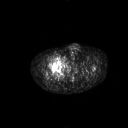
FDG PET of an extremity soft-tissue mass (from a PET/CT study), one axial slice. Position 287 of 311 along the scan axis. 128 × 128 image matrix, field of view 700 × 700 mm. Male patient, age 50 years. Case-level facts recorded for this patient, not image findings: histological type: undifferentiated - pleiomorphic; grade: high; site of the primary tumour: right thigh.
Annotated regions visible in this slice (expert contour drawn on MRI and transferred to this co-registered scan by the dataset authors):
- gross tumour volume including surrounding oedema: box from (x=53, y=55) to (x=65, y=67) px
- gross tumour volume (mass): (x=53, y=56)–(x=63, y=66)